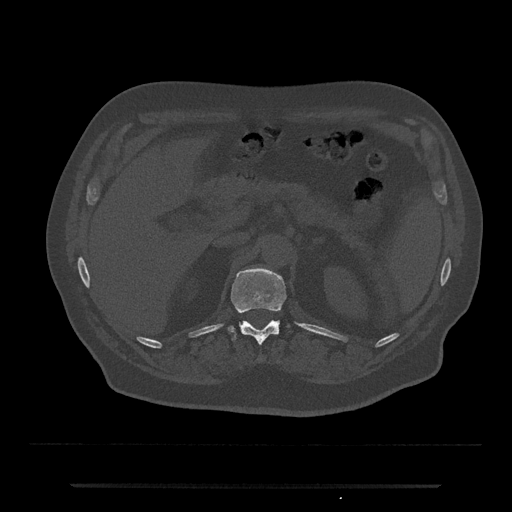
CT including the spine, one axial slice; reconstruction kernel Br40s/3; bone window (W 1800 / L 400 HU); 0.5 mm slice thickness; 512 × 512 image matrix, field of view 434 × 434 mm. Patient: male, 80 years. Case-level facts recorded for this patient, not image findings: primary cancer: prostate.
Outlined on this slice (semi-automatic segmentation, software-assisted and operator-edited):
- T12 vertebra: bounding box [x1, y1, x2, y2] px = [228, 268, 287, 346]